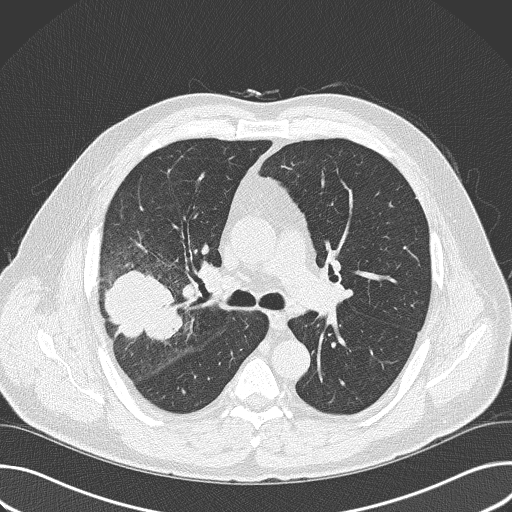
Chest CT (low-dose screening protocol), one axial image. First (baseline) screen. Lung window (W 1500 / L -600 HU). 512 × 512 image matrix, field of view 380 × 380 mm. Male participant, aged 56 years at enrolment.
Expert reader's lesion annotation, bounding box [x1, y1, x2, y2] px = [81, 261, 185, 367]. The exam's reader record, not a measurement of the box and not confirmed to be the same lesion: non-calcified nodule or mass ≥4 mm, right upper lobe, 6 × 5 mm, spiculated (stellate) margins, soft tissue attenuation. Later outcome: lung cancer diagnosed 16 days after this screen — adenocarcinoma, NOS, right upper lobe, poorly differentiated (G3), stage IIB (AJCC 6th edition), 60 mm at pathology.